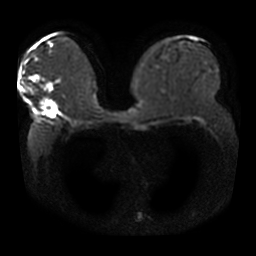
Breast MRI, one axial slice; slice 22 of 42 in the series (ordered by position); diffusion-weighted series; image 2 of 4 stored at this slice position (different b-values; order by instance number); 3 T; 5 mm slice thickness; 256 × 256 image matrix, field of view 360 × 360 mm. Female patient.
Outlined on this slice (manually delineated by an expert):
- tumour on diffusion-weighted imaging: box from (x=42, y=101) to (x=57, y=118) px